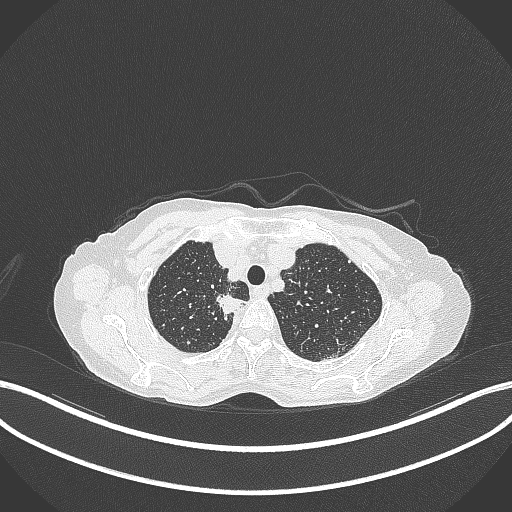
Chest CT, one axial slice; position 313 of 403 along the scan axis; reconstruction kernel B70f; lung window (W 1500 / L -600 HU); 1 mm slice thickness; 512 × 512 image matrix. Female patient, age 75 years. From the clinical record (not read from this slice): clinical TNM (as recorded): T1c N1 M1.
Structures marked on this image (bounding box drawn by a radiologist):
- lung tumour (recorded histology: adenocarcinoma): box from (x=212, y=290) to (x=247, y=318) px